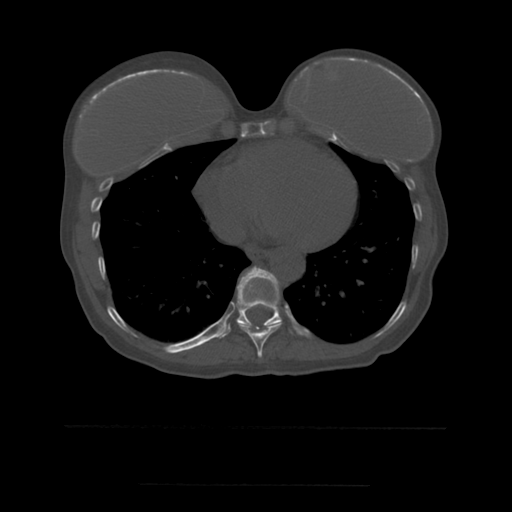
CT including the spine, one axial slice; slice 312 of 544 in the series (ordered by position); bone window (W 1800 / L 400 HU); 512 × 512 image matrix, field of view 350 × 350 mm. Patient age 58 years. Case-level facts recorded for this patient, not image findings: primary cancer: lung.
Structures marked on this image (semi-automatic segmentation, software-assisted and operator-edited):
- T10 vertebra: bounding box (x1, y1, x2, y2) in pixels: (216, 267, 282, 338)
- T9 vertebra: (237, 276, 282, 358)